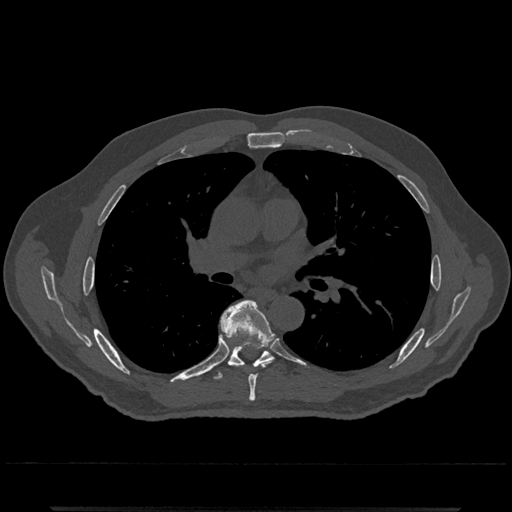
CT including the spine, one axial slice; slice 749 of 797 in the series (ordered by position); reconstruction kernel Br40s/3; 120 kVp; bone window (W 1800 / L 400 HU); 0.5 mm slice thickness; 512 × 512 image matrix, field of view 393 × 393 mm. Male patient, age 67 years. From the clinical record (not read from this slice): primary cancer: prostate.
Structures marked on this image (semi-automatic segmentation, software-assisted and operator-edited):
- T6 vertebra: bounding box [x1, y1, x2, y2] px = [221, 300, 274, 402]
- T7 vertebra: [212, 331, 273, 380]